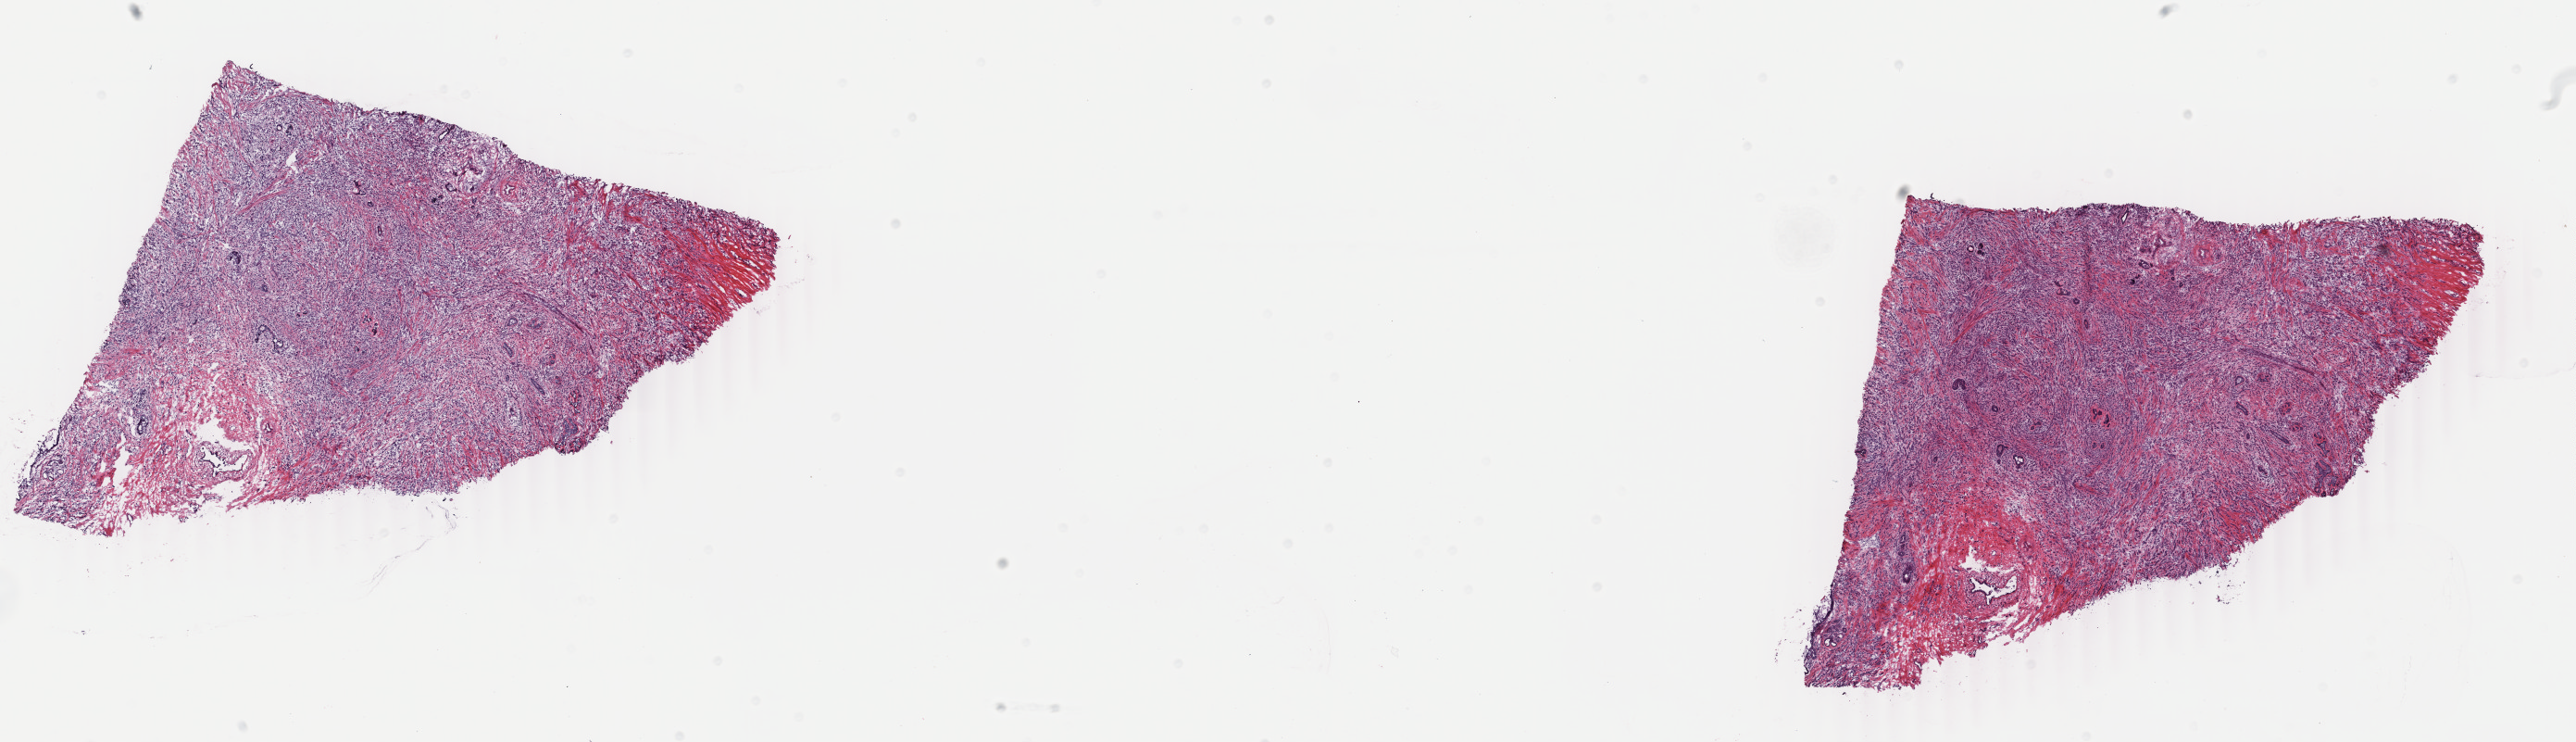
Digitized H&E-stained tissue section (whole slide) — whole scanned area (about 22.1 x 6.4 mm, acquisition: 40x scan) shown as a low-resolution overview; frozen section from the bottom of the tissue portion; primary tumour sample from the breast. Female patient; age at initial diagnosis 48 years. Composition of this section per pathologist review: tumour cells 85%, tumour nuclei 95%, normal cells 5%, stromal cells 10%, necrosis 0%. Infiltration values recorded for this section: lymphocyte infiltration 0%, monocyte infiltration 0%, neutrophil infiltration 0%.
• AJCC pathologic stage: IIIA
• lymph nodes positive (case pathology): 4 of 29 examined
• diagnosis: Lobular carcinoma, NOS